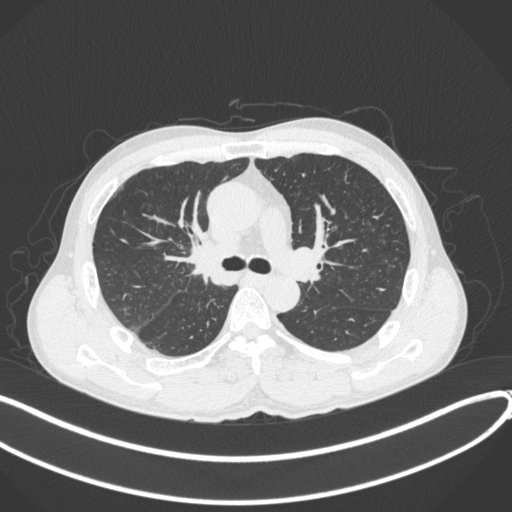
Chest CT, one axial slice; slice 244 of 409 in the series (ordered by position); reconstruction kernel B31f; 120 kVp; lung window (W 1500 / L -600 HU); 1 mm slice thickness; 512 × 512 image matrix, field of view 400 × 400 mm. Male patient, age 53 years. From the clinical record (not read from this slice): clinical TNM (as recorded): T1b N0 M0.
Outlined on this slice (rectangle marked by the reading radiologist):
- lung tumour (recorded histology: squamous cell carcinoma): bounding box [x1, y1, x2, y2] px = [177, 232, 230, 291]